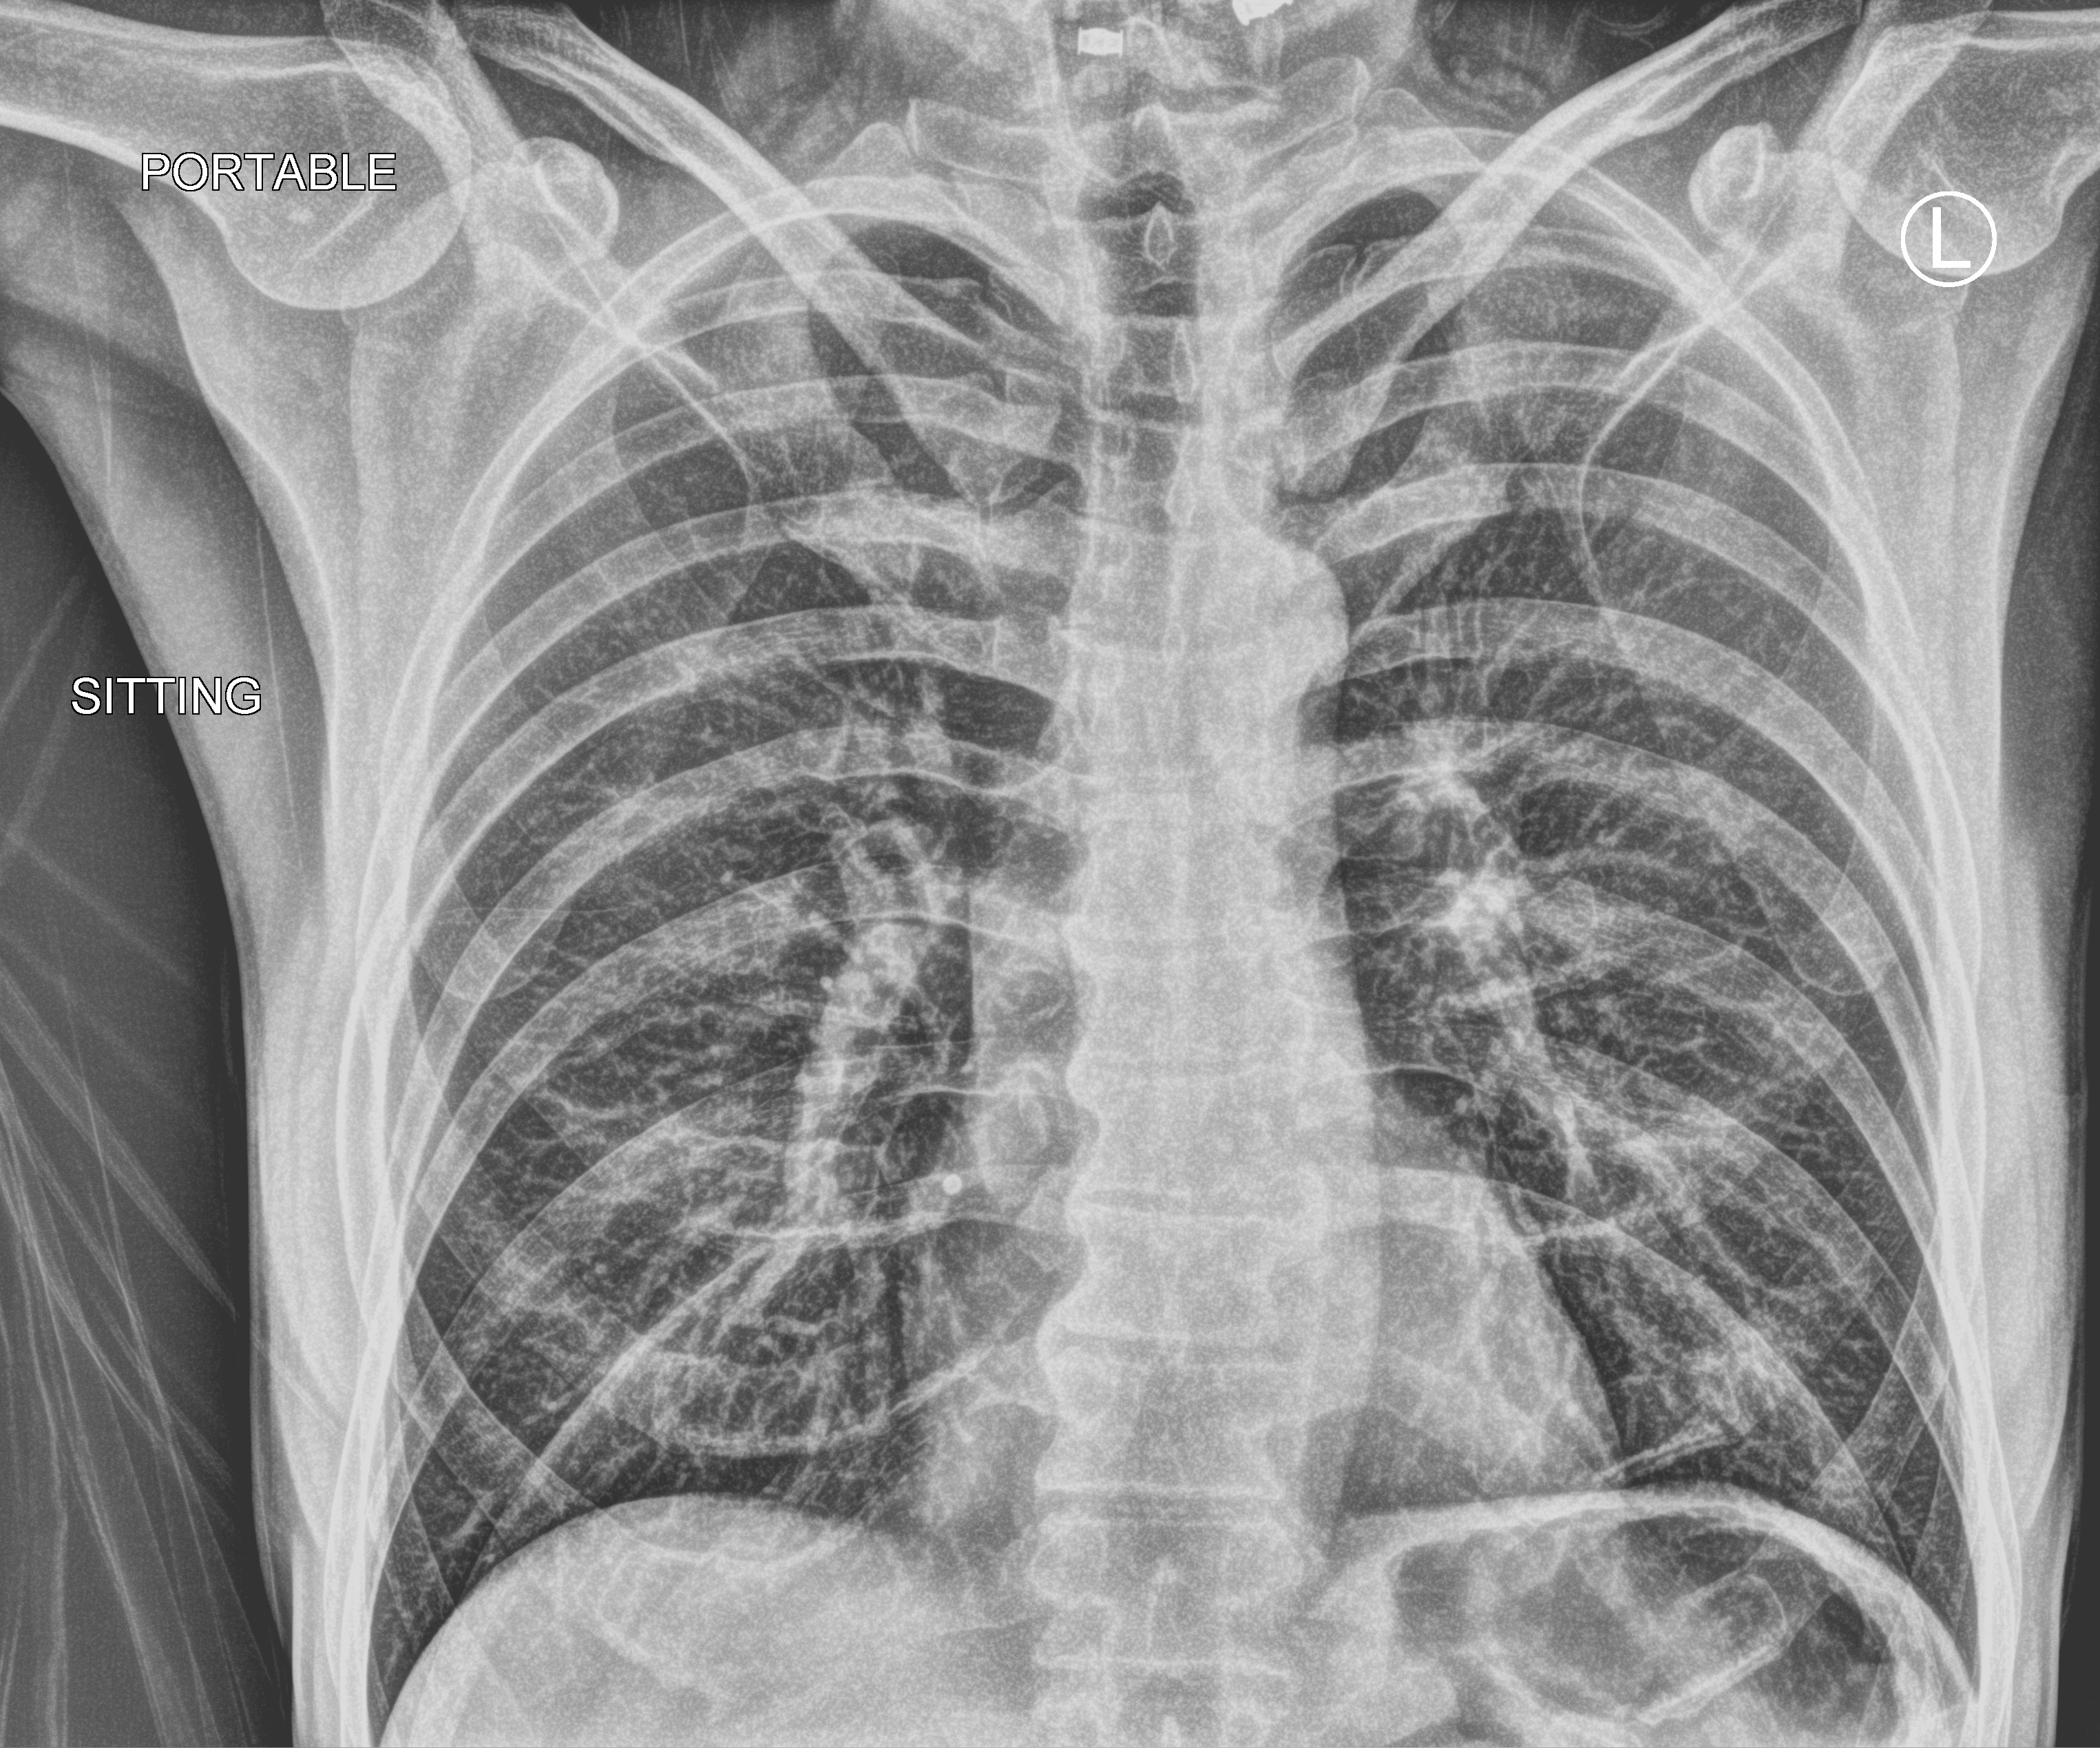
Portable chest radiograph; anteroposterior (AP) projection. Patient hospitalised with COVID-19; male, aged 18–59 years.
Admission-level facts for this patient (not findings on this image; timing relative to this image not recorded): admitted to intensive care during this hospital stay: no.